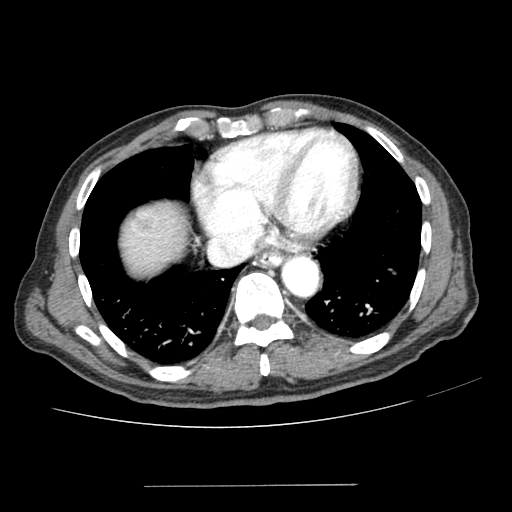
Contrast-enhanced abdominal CT (liver protocol), one axial slice. Position 180 of 187 along the scan axis. 100 kVp. Soft-tissue window (W 400 / L 40 HU). 2.5 mm slice thickness. 512 × 512 image matrix. From the clinical record (not read from this slice): diagnosis: hepatocellular carcinoma (patient treated with transarterial chemoembolisation; whether this scan precedes or follows treatment is not stated here); TNM stage (as recorded): Stage-I; Child-Pugh class: A; tumour size: 1.6 cm.
Outlined on this slice (semi-automatic segmentation, software-assisted and operator-edited):
- liver parenchyma outside the tumour (the mass and vessels are separate outlines, so this box may not span the whole liver): bounding box (x1, y1, x2, y2) in pixels: (122, 202, 186, 272)